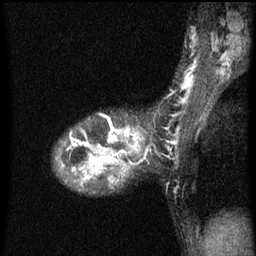
Breast MRI (dynamic contrast-enhanced), one sagittal slice; slice 39 of 60 in the series (ordered by position); dynamic contrast-enhanced series, image 2 of 3 at this slice position (ordered by acquisition); 1.5 T; TE 4.2 ms, TR 8 ms; 256 × 256 image matrix. Female patient, age 36 years.
Structures marked on this image (semi-automatically segmented with operator editing):
- analysis volume of interest (the breast-tissue region the enhancement analysis was run in; not a lesion): box from (x=62, y=132) to (x=129, y=161) px
- tumour enhancement mask (voxels above the 70 % enhancement threshold inside the analysis volume of interest): (x=70, y=132)–(x=129, y=161)